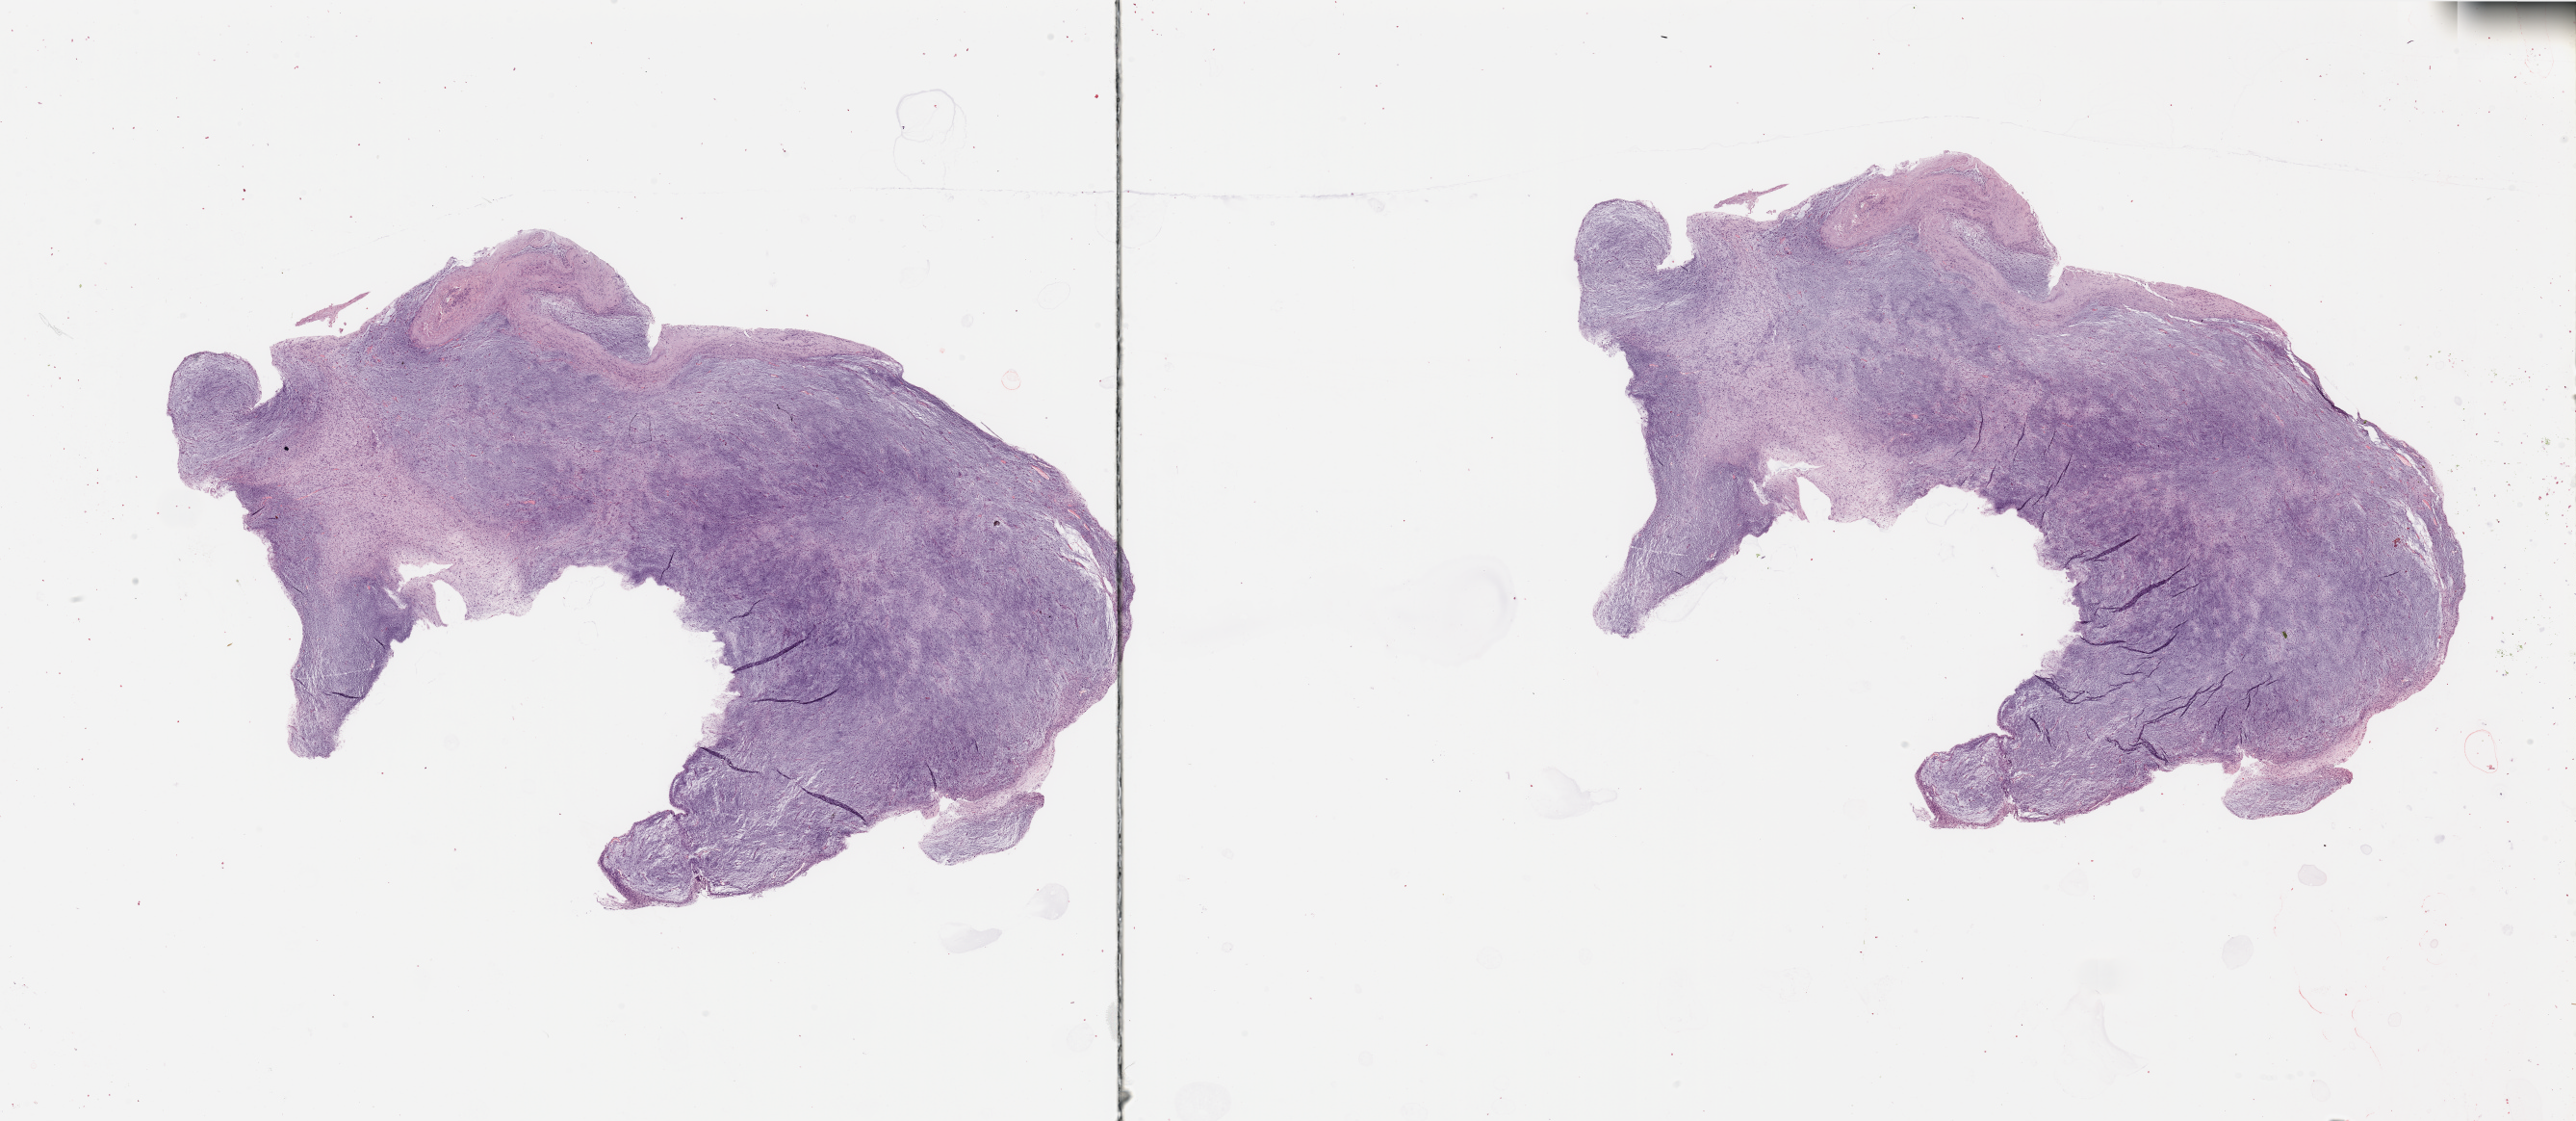
Digitized Hematoxylin and eosin (H&E) stained tissue section (whole slide) — low-resolution overview of the scanned area, about 42.3 x 18.4 mm (from a 20x scan); tumour tissue sample. Patient: male, age 70 years.
- primary tumour site (as recorded): lower extremity
- patient diagnosis (cohort enrolment): sarcoma (site not recorded at cohort level)